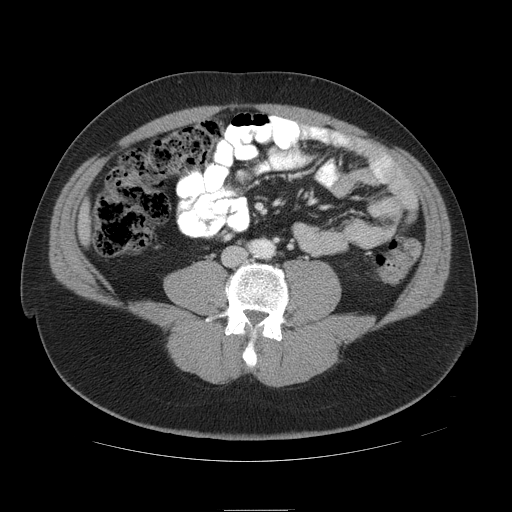
Contrast-enhanced abdominal CT, one axial slice. Position 8 of 49 along the scan axis. Reconstruction kernel STANDARD. 120 kVp. Intravenous contrast given. Soft-tissue window (W 400 / L 40 HU). 5 mm slice thickness. 512 × 512 image matrix. Male patient, age 52 years. Case-level facts recorded for this patient, not image findings: diagnosis: colorectal cancer liver metastases, imaged before liver resection.
Structures marked on this image (manually delineated by an expert):
- liver: bounding box <83,216,85,230> (left, top, right, bottom; pixels)